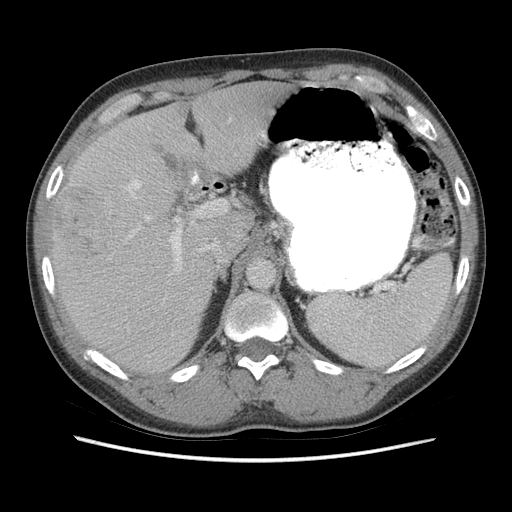
Contrast-enhanced abdominal CT (liver protocol), one axial slice; slice 43 of 73 in the series (ordered by position); soft-tissue window (W 400 / L 40 HU); 2.5 mm slice thickness; 512 × 512 image matrix, field of view 360 × 360 mm. Case-level facts recorded for this patient, not image findings: diagnosis: hepatocellular carcinoma (patient treated with transarterial chemoembolisation; whether this scan precedes or follows treatment is not stated here); TNM stage (as recorded): Stage-IIIA; Child-Pugh class: A; tumour nodularity: multinodular; tumour size: 6.6 cm.
Annotated regions visible in this slice (semi-automatically segmented with operator editing):
- liver parenchyma outside the tumour (the mass and vessels are separate outlines, so this box may not span the whole liver): box from (x=50, y=80) to (x=293, y=372) px
- mass: (x=57, y=188)–(x=113, y=257)
- liver vessels: (x=127, y=134)–(x=265, y=275)